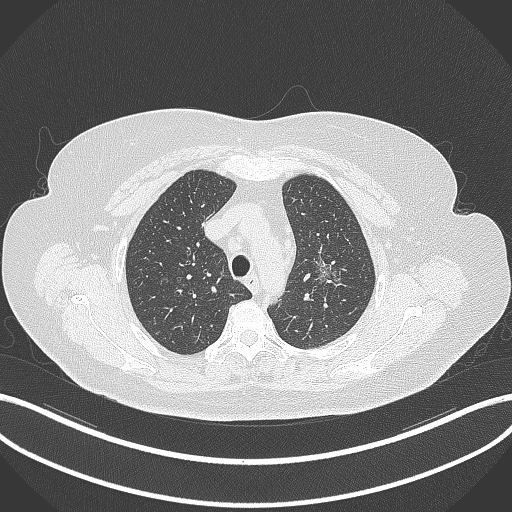
Chest CT, one axial slice. Slice 261 of 309 in the series (ordered by position). Reconstruction kernel B70f. 120 kVp. Lung window (W 1500 / L -600 HU). 1 mm slice thickness. 512 × 512 image matrix, field of view 400 × 400 mm. Female patient, age 70 years. From the clinical record (not read from this slice): clinical TNM (as recorded): T1c N0 M0.
Outlined on this slice (bounding box drawn by a radiologist):
- lung tumour (recorded histology: adenocarcinoma): box from (x=308, y=246) to (x=350, y=294) px